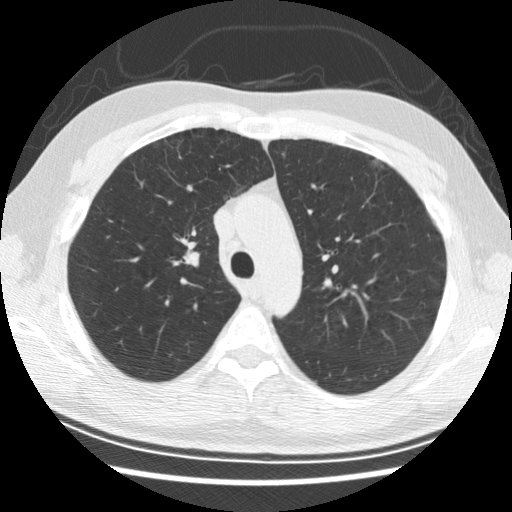
Chest CT (low-dose screening protocol), one axial image. Baseline annual screen. Lung window (W 1500 / L -600 HU). 512 × 512 image matrix. Male participant, aged 57 years at enrolment. Former smoker at enrolment.
- Expert-annotated lung lesion, box from (x=162, y=221) to (x=219, y=282) px.
- The screening reader recorded 6 non-calcified nodules or masses ≥4 mm on this exam (right middle lobe, right middle lobe, right lower lobe, right middle lobe, right middle lobe, right lower lobe); which of them this box marks is not recorded.
- Official screen result: negative screen, minor abnormalities not suspicious for lung cancer.
- Later outcome: lung cancer diagnosed 766 days after this screen — adenocarcinoma, NOS, right upper lobe, poorly differentiated (G3), stage IB (AJCC 6th edition), 25 mm at pathology.